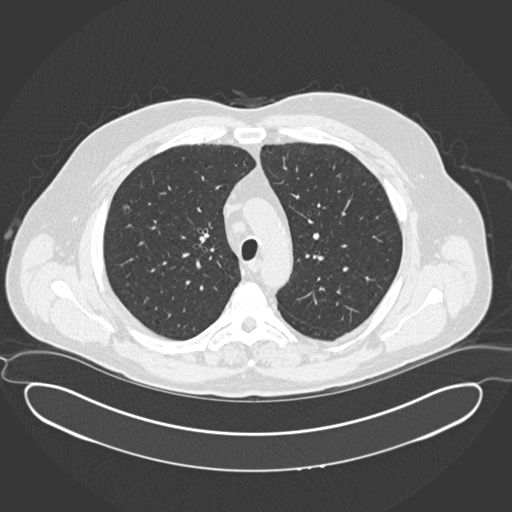
Low-dose screening chest CT, one axial slice; position 122 of 169 along the scan axis; reconstruction kernel B30f; 120 kVp; lung window (W 1500 / L -600 HU); 512 × 512 image matrix, field of view 446 × 446 mm.
Annotated regions visible in this slice (expert manual segmentation):
- lesion 1 (tumor, upper lobe of right lung): box from (x=124, y=205) to (x=129, y=209) px